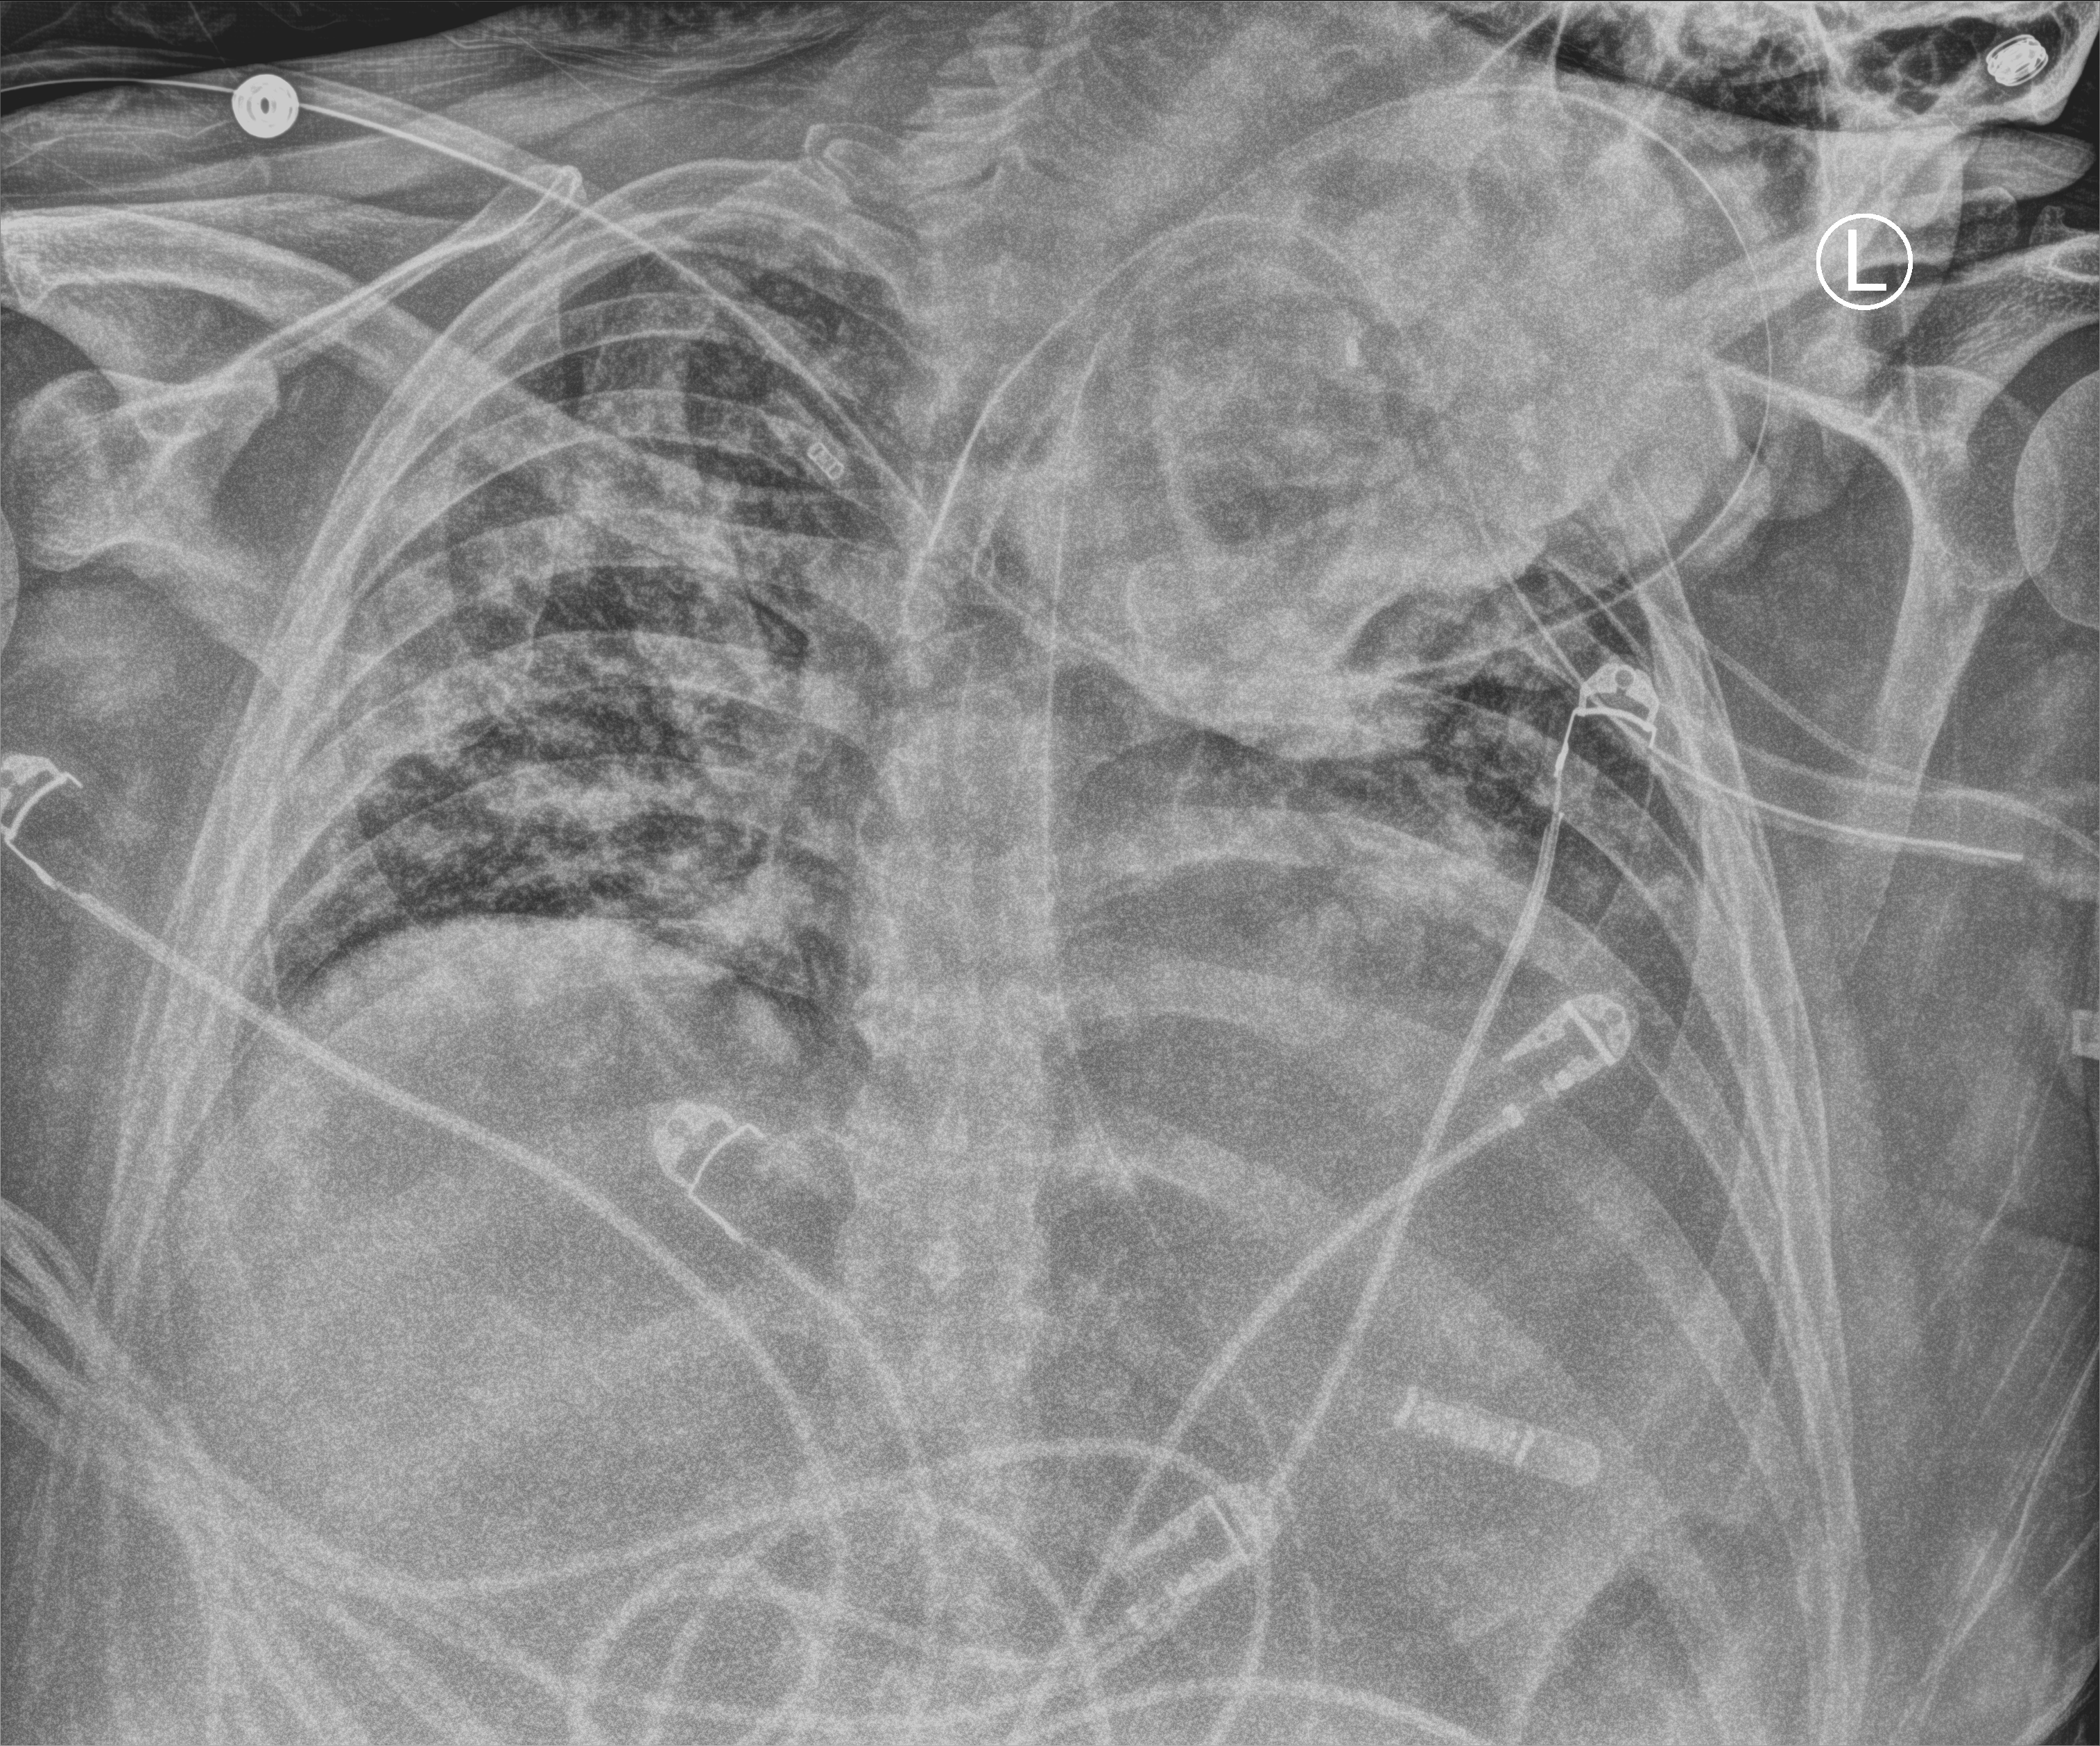
Bedside chest radiograph (computed radiography); anteroposterior (AP) projection. Male patient hospitalised with COVID-19, age 18–59 years.
Admission-level facts for this patient (not findings on this image; timing relative to this image not recorded): mechanically ventilated during this hospital stay: yes; length of hospital stay: 39 days.